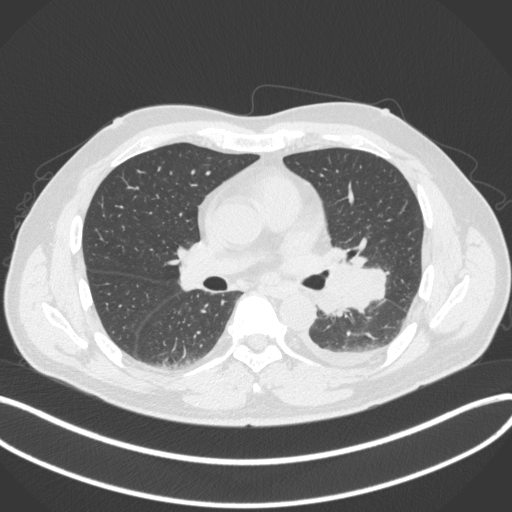
Chest CT, one axial slice. Slice 196 of 350 in the series (ordered by position). Reconstruction kernel B31f. 120 kVp. Lung window (W 1500 / L -600 HU). 1 mm slice thickness. 512 × 512 image matrix, field of view 400 × 400 mm. Patient: male, 58 years. From the clinical record (not read from this slice): clinical TNM (as recorded): T3 N1 M1b; histopathological grade: G3.
Structures marked on this image (rectangle marked by the reading radiologist):
- lung tumour (recorded histology: small cell carcinoma): bounding box [x1, y1, x2, y2] px = [315, 260, 389, 320]